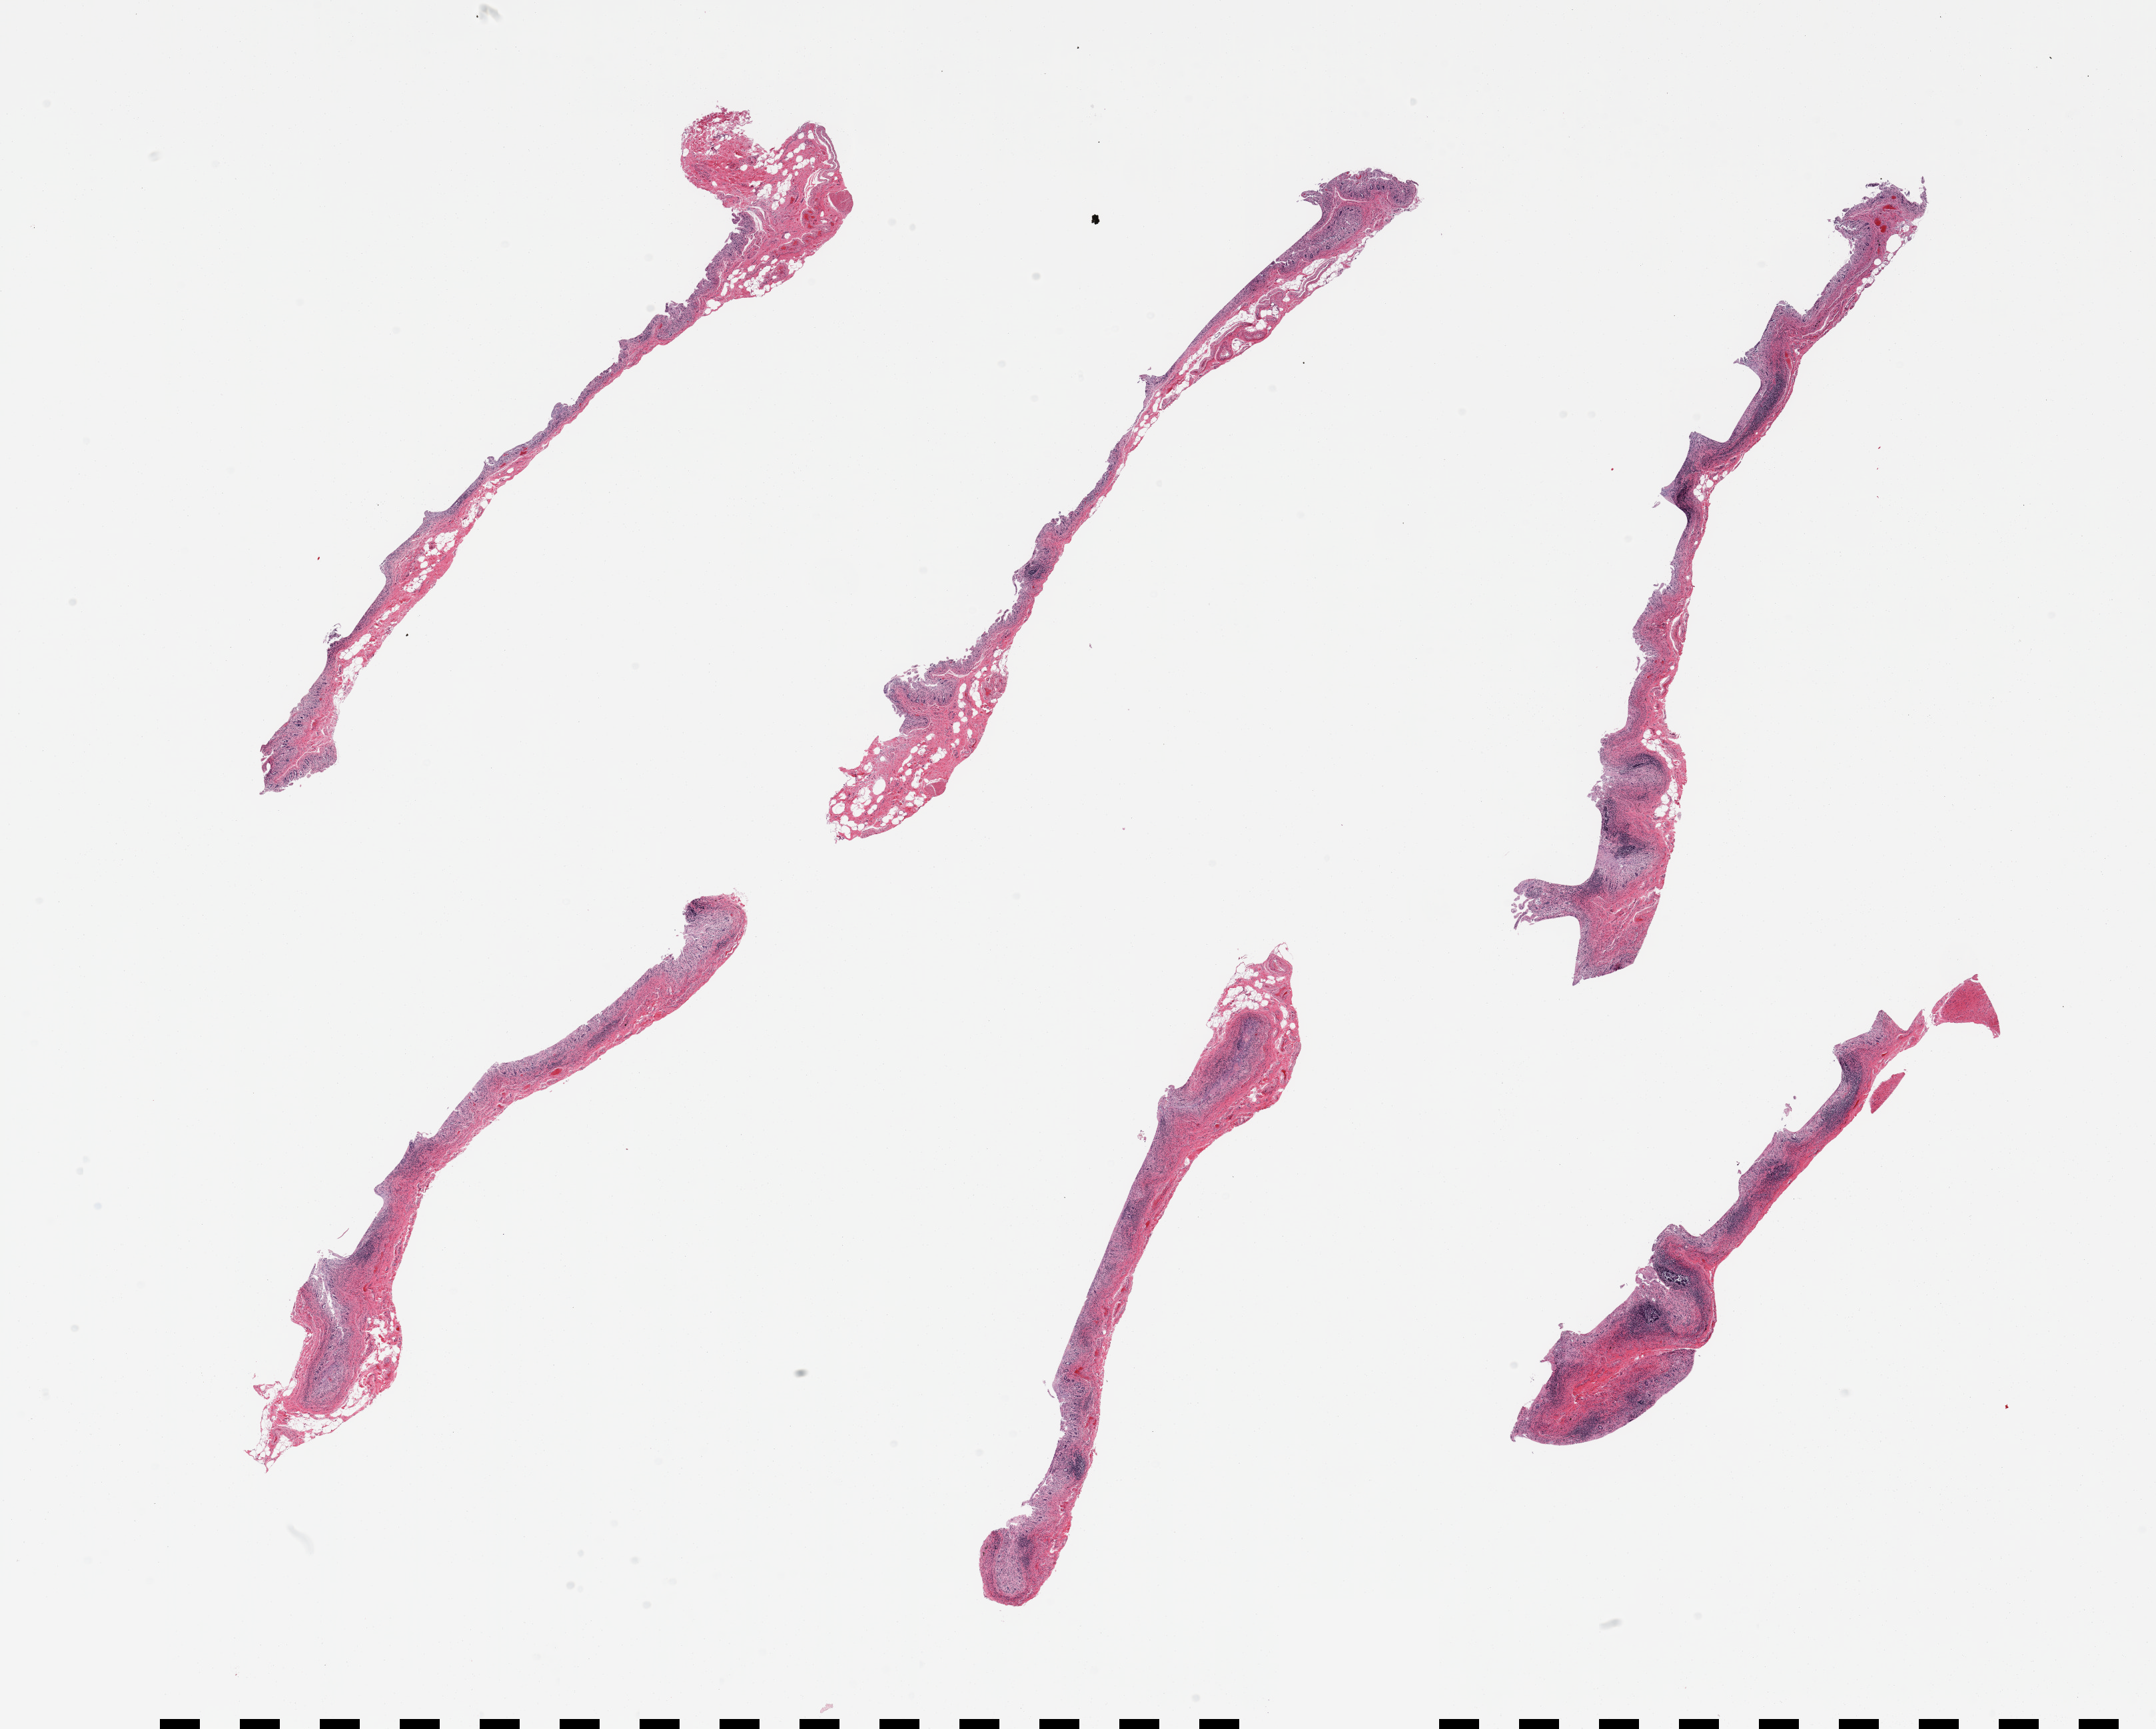
Digitized hematoxylin and eosin (H&E)-stained section — shown as a low-resolution overview of the whole scanned area (about 25.6 x 20.5 mm). Donor: male.
* specimen: PAXgene-fixed paraffin-embedded (PFPE) section; section of ileum (target tissue); donor tissue sample